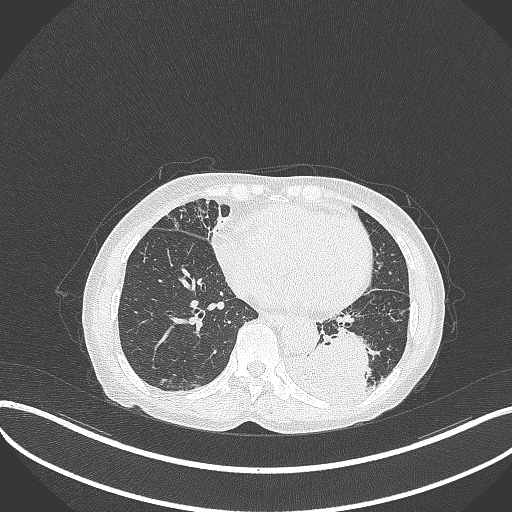
Chest CT, one axial slice; reconstruction kernel B70f; 120 kVp; lung window (W 1500 / L -600 HU); 1 mm slice thickness; 512 × 512 image matrix. Female patient, age 78 years. Case-level facts recorded for this patient, not image findings: clinical TNM (as recorded): T3 N0 M1.
Annotated regions visible in this slice (bounding box drawn by a radiologist):
- lung tumour (recorded histology: squamous cell carcinoma): bounding box [x1, y1, x2, y2] px = [281, 332, 371, 402]